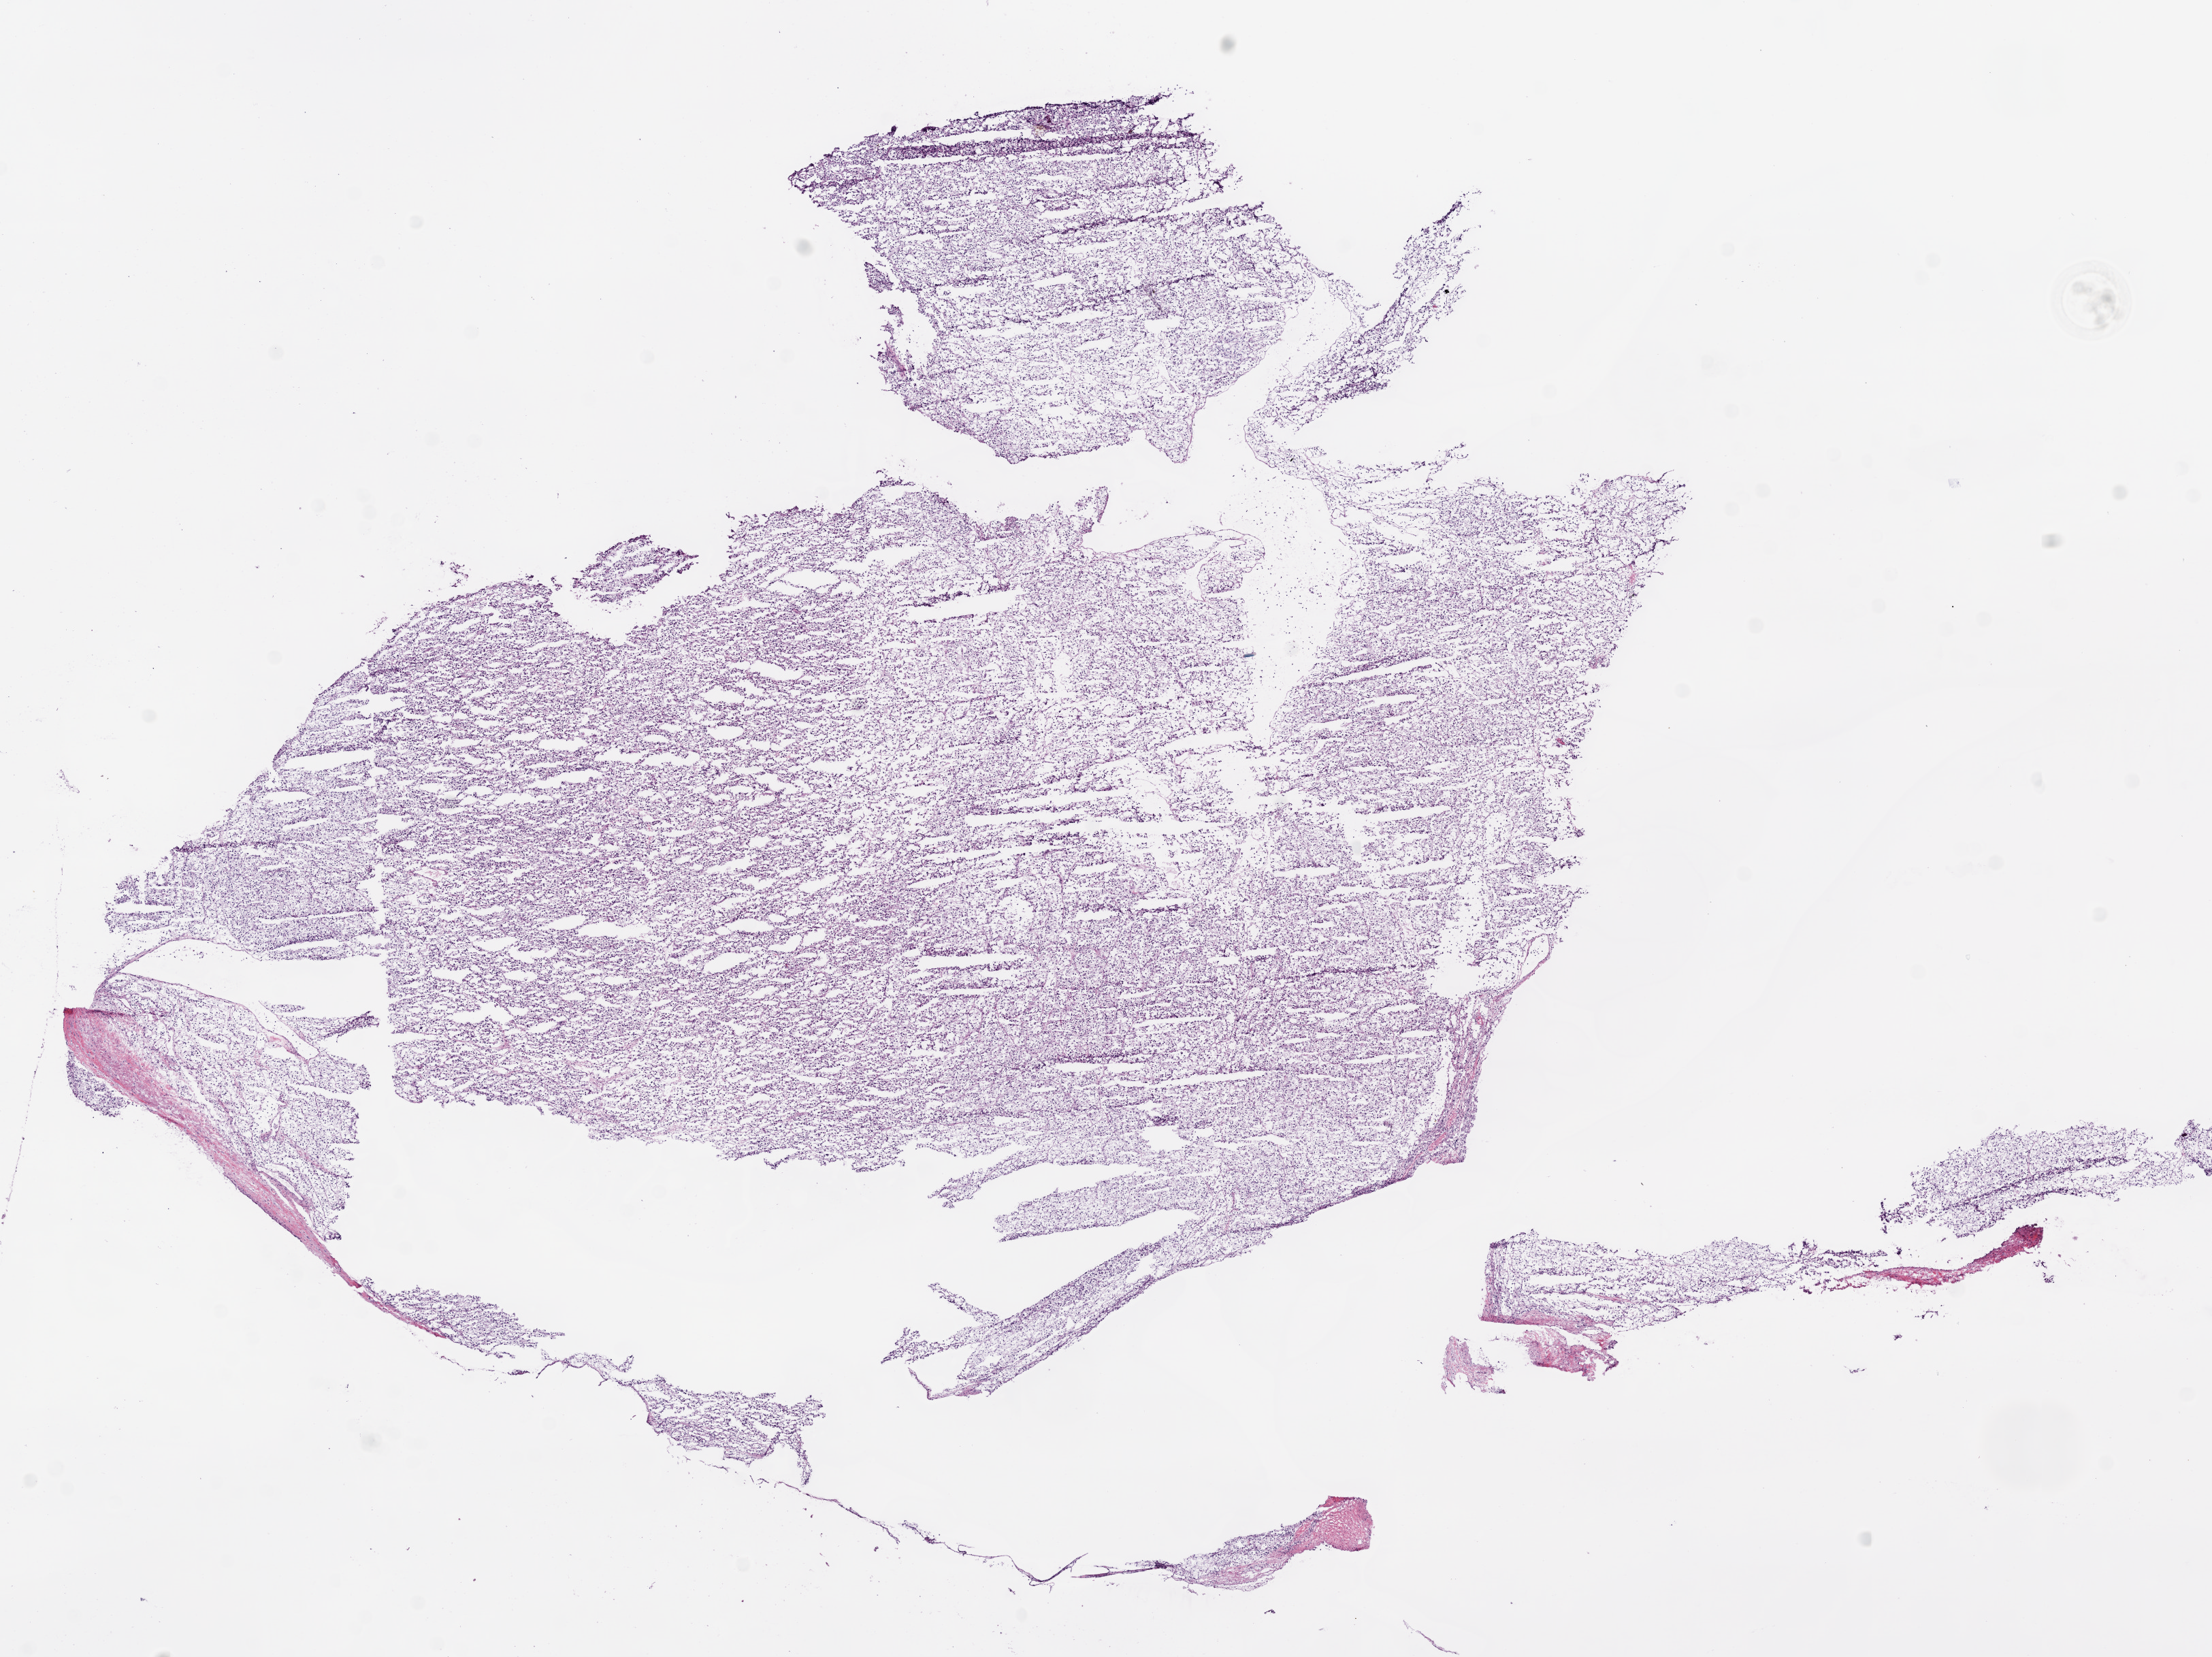
Digitized H&E tissue section (whole slide) — a low-resolution overview of the entire scanned area, about 13.0 x 9.8 mm (from a 20x scan), frozen section from the bottom of the tissue portion, primary tumour sample from the kidney. Female patient; age at initial diagnosis 64 years. Histologic grade: G2 (moderately differentiated). Slide review estimates, as recorded: tumour cells 95%, tumour nuclei 90%, normal cells 0%, stromal cells 5%, necrosis 0%.
* AJCC pathologic stage: I
* histologic diagnosis: Clear cell adenocarcinoma, NOS